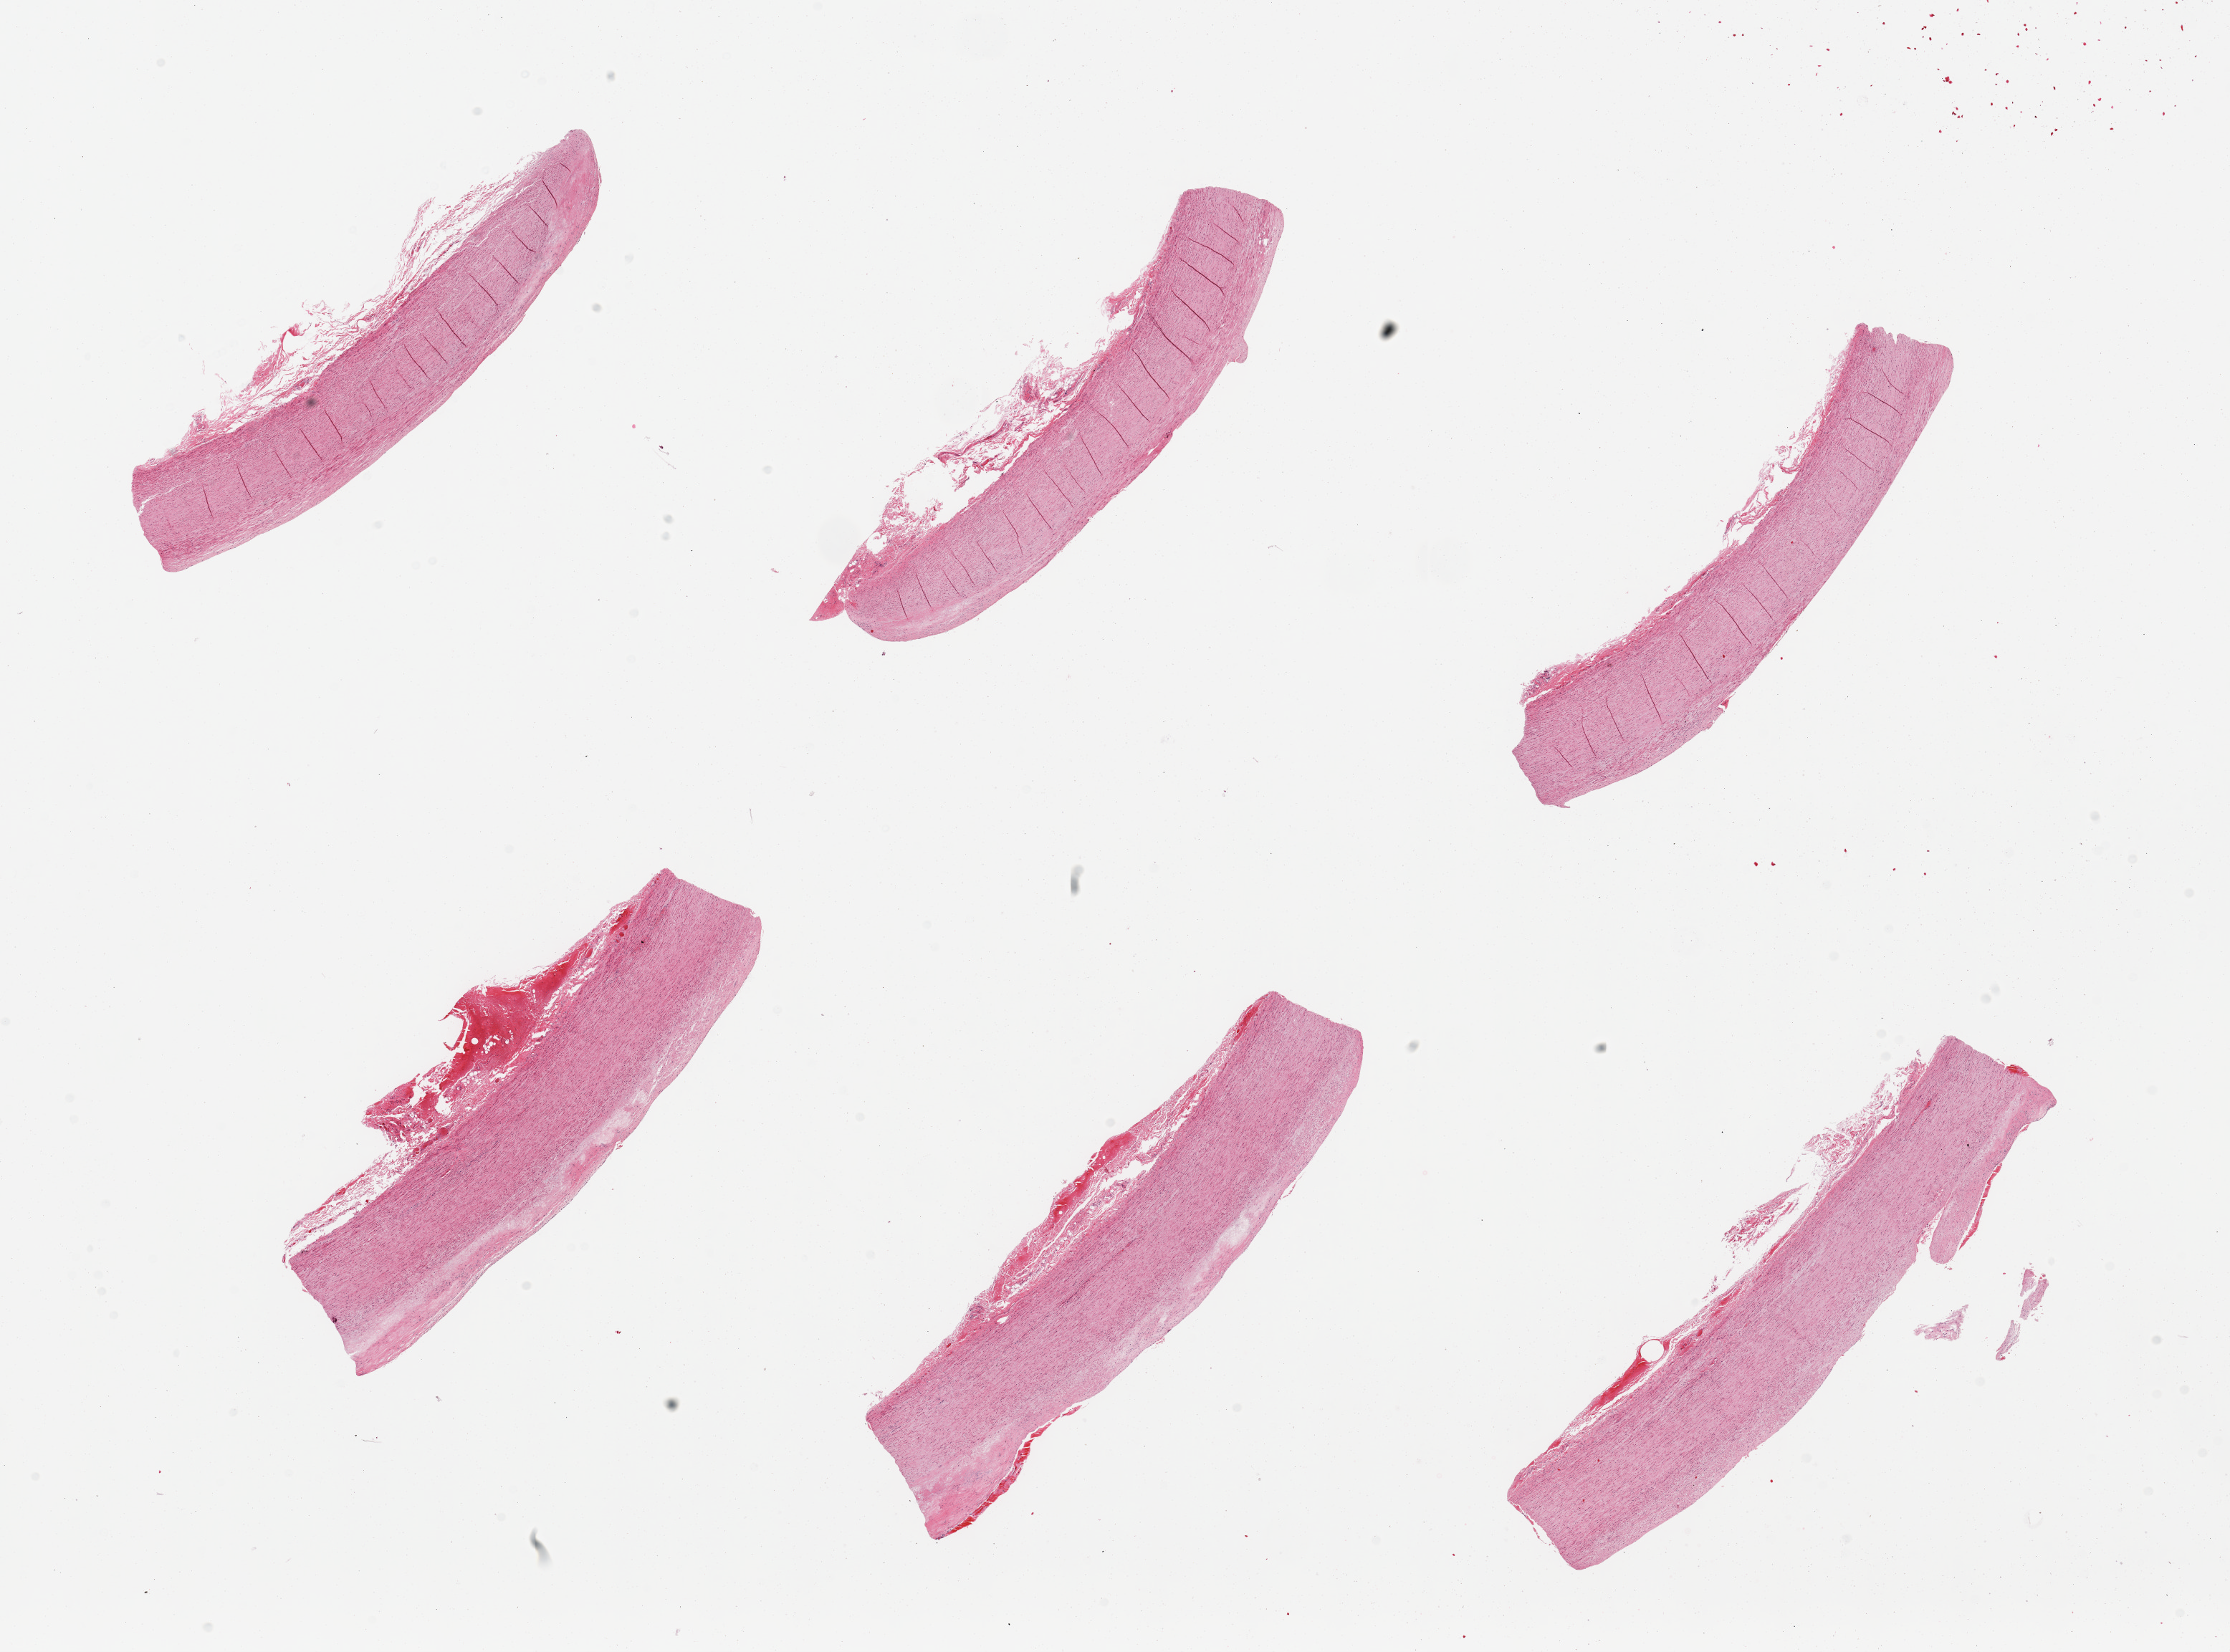
H&E whole-slide image, shown as a low-resolution overview of the whole scanned area (about 24.6 x 18.2 mm, acquisition: 20x scan); PAXgene-fixed, paraffin-embedded tissue; section of aorta (target tissue); donor tissue sample. Donor: male.
- reviewer comment on this tissue sample: 6 pieces, up to ~0.2mm atherosis